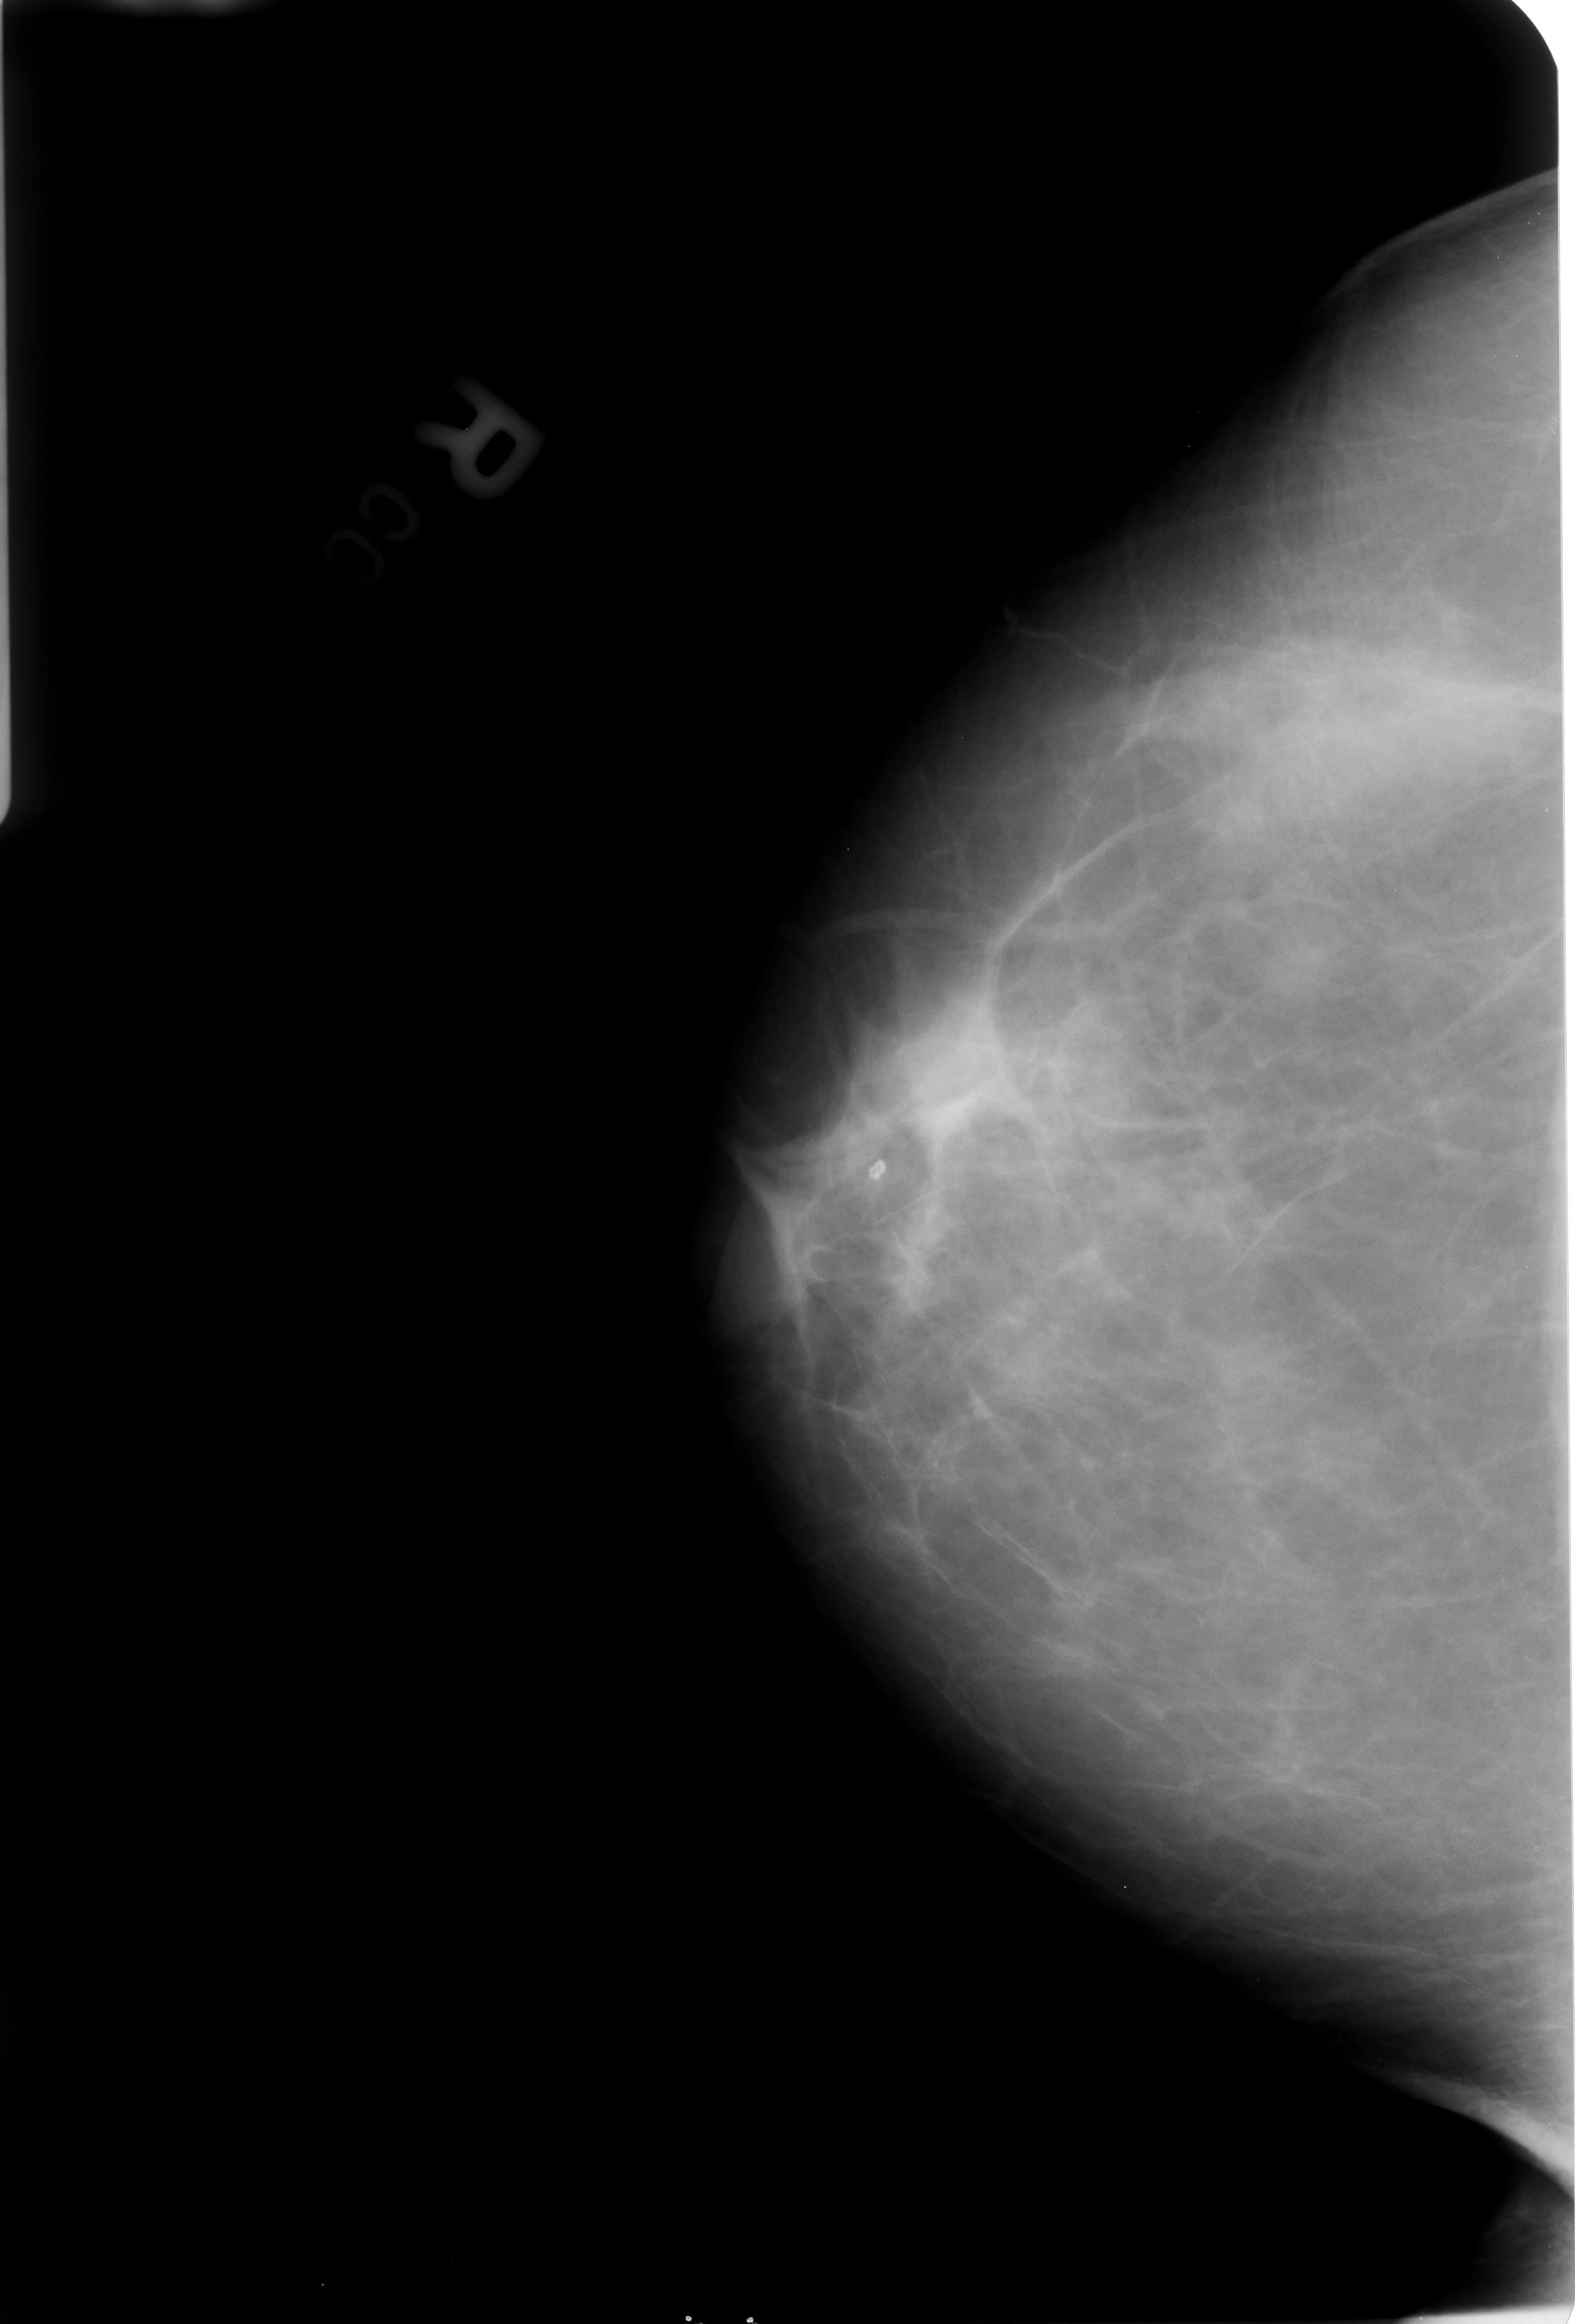
Mammogram (digitized film). Right breast. CC view. BI-RADS breast density category 2 (scale 1–4). 1575 × 2324 image matrix.
Marked abnormalities (boxes around the expert regions of interest):
- calcifications, morphology lucent center; BI-RADS assessment category 2; subtlety rating 5 on a 1 (subtle) to 5 (obvious) scale; benign; no additional work-up was recommended (outcome (as recorded, no biopsy): benign without callback): bounding box (x1, y1, x2, y2) in pixels: (857, 1151, 895, 1201)